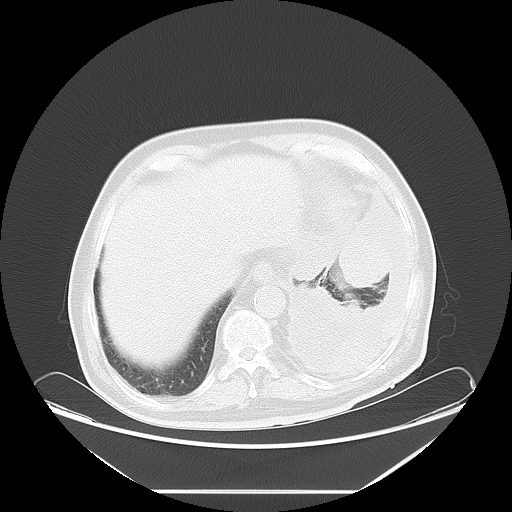
Chest CT, one axial slice; slice 15 of 63 in the series (ordered by position); 120 kVp; lung window (W 1500 / L -600 HU); 5 mm slice thickness; 512 × 512 image matrix, field of view 448 × 448 mm. Male patient, age 67 years. From the clinical record (not read from this slice): clinical TNM (as recorded): T1b N1 M1a; histopathological grade: G3.
Outlined on this slice (bounding box drawn by a radiologist):
- lung tumour (recorded histology: small cell carcinoma): bounding box [x1, y1, x2, y2] px = [337, 232, 394, 289]